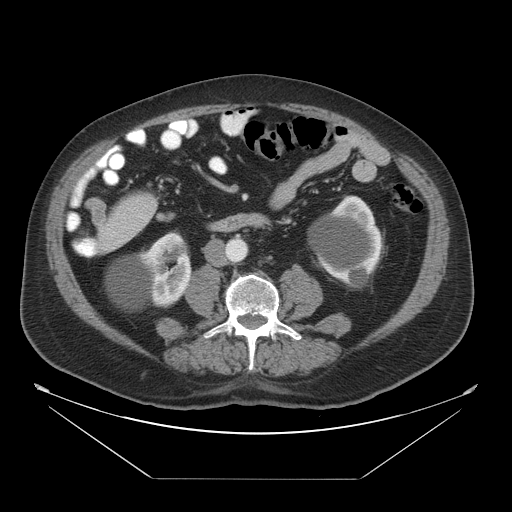
Contrast-enhanced abdominal CT, one axial slice. Position 9 of 45 along the scan axis. Intravenous contrast given. Soft-tissue window (W 400 / L 40 HU). 5 mm slice thickness. 512 × 512 image matrix, field of view 463 × 463 mm. Male patient, age 87 years. From the clinical record (not read from this slice): diagnosis: colorectal cancer liver metastases, imaged before liver resection; multiple liver metastases: no; largest metastasis: 4.5 cm.
Annotated regions visible in this slice (expert manual segmentation):
- liver: bounding box (x1, y1, x2, y2) in pixels: (98, 192, 158, 253)